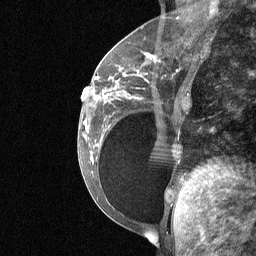
Breast MRI (dynamic contrast-enhanced), one sagittal slice. Position 24 of 64 along the scan axis. Dynamic contrast-enhanced study with each time point stored as its own series, time point 2 of 3 at this slice position (early post-contrast, ordered by acquisition time). 1.5 T. TE 4.8 ms, TR 27 ms. 2 mm slice thickness. 256 × 256 image matrix, field of view 200 × 200 mm. Female patient, age 34 years. Case-level facts recorded for this patient, not image findings: setting: breast cancer imaged before/during neoadjuvant chemotherapy; receptor status: HR-positive, HER2-negative.
Outlined on this slice (semi-automatically segmented with operator editing):
- analysis volume of interest (the breast-tissue region the enhancement analysis was run in; not a lesion): bounding box [x1, y1, x2, y2] px = [92, 50, 188, 185]
- tumour enhancement mask (voxels above the 90 % enhancement threshold inside the analysis volume of interest): [96, 53, 152, 98]